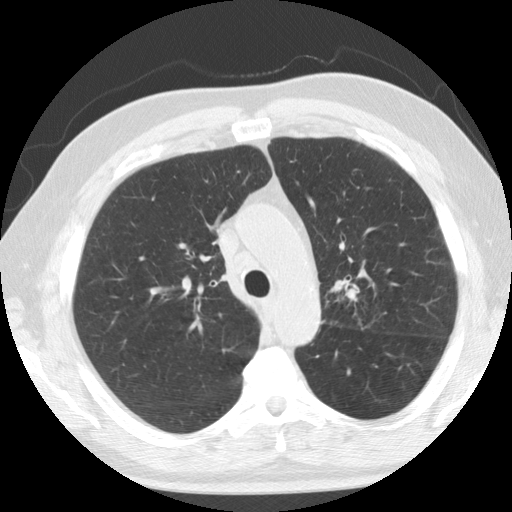
Chest CT (low-dose screening protocol), one axial image; second annual screen; lung window (W 1500 / L -600 HU); 120 kVp; slice 41 of 133 in the series; 512 × 512 image matrix, field of view 342 × 342 mm. Male participant, aged 74 years at enrolment.
Expert reader's lesion annotation, bounding box [x1, y1, x2, y2] px = [305, 264, 373, 328]. Screening reader's record for this exam: no non-calcified nodule ≥4 mm recorded.